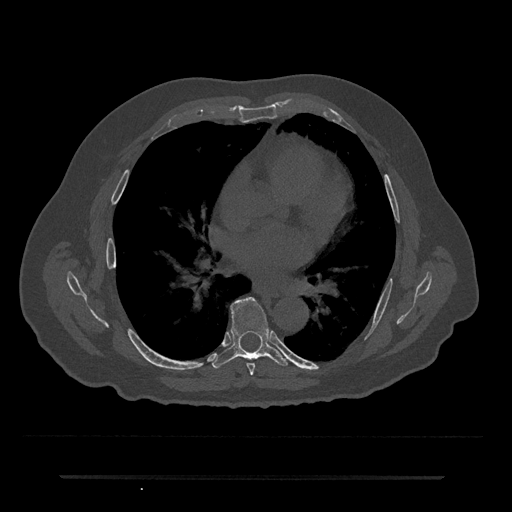
CT including the spine, one axial slice; slice 401 of 797 in the series (ordered by position); reconstruction kernel Br40s/3; 120 kVp; bone window (W 1800 / L 400 HU); 512 × 512 image matrix, field of view 437 × 437 mm. Patient: male, 69 years. From the clinical record (not read from this slice): primary cancer: prostate.
Annotated regions visible in this slice (semi-automatically segmented with operator editing):
- T6 vertebra: bounding box (x1, y1, x2, y2) in pixels: (247, 363, 255, 375)
- T7 vertebra: (212, 297, 288, 369)